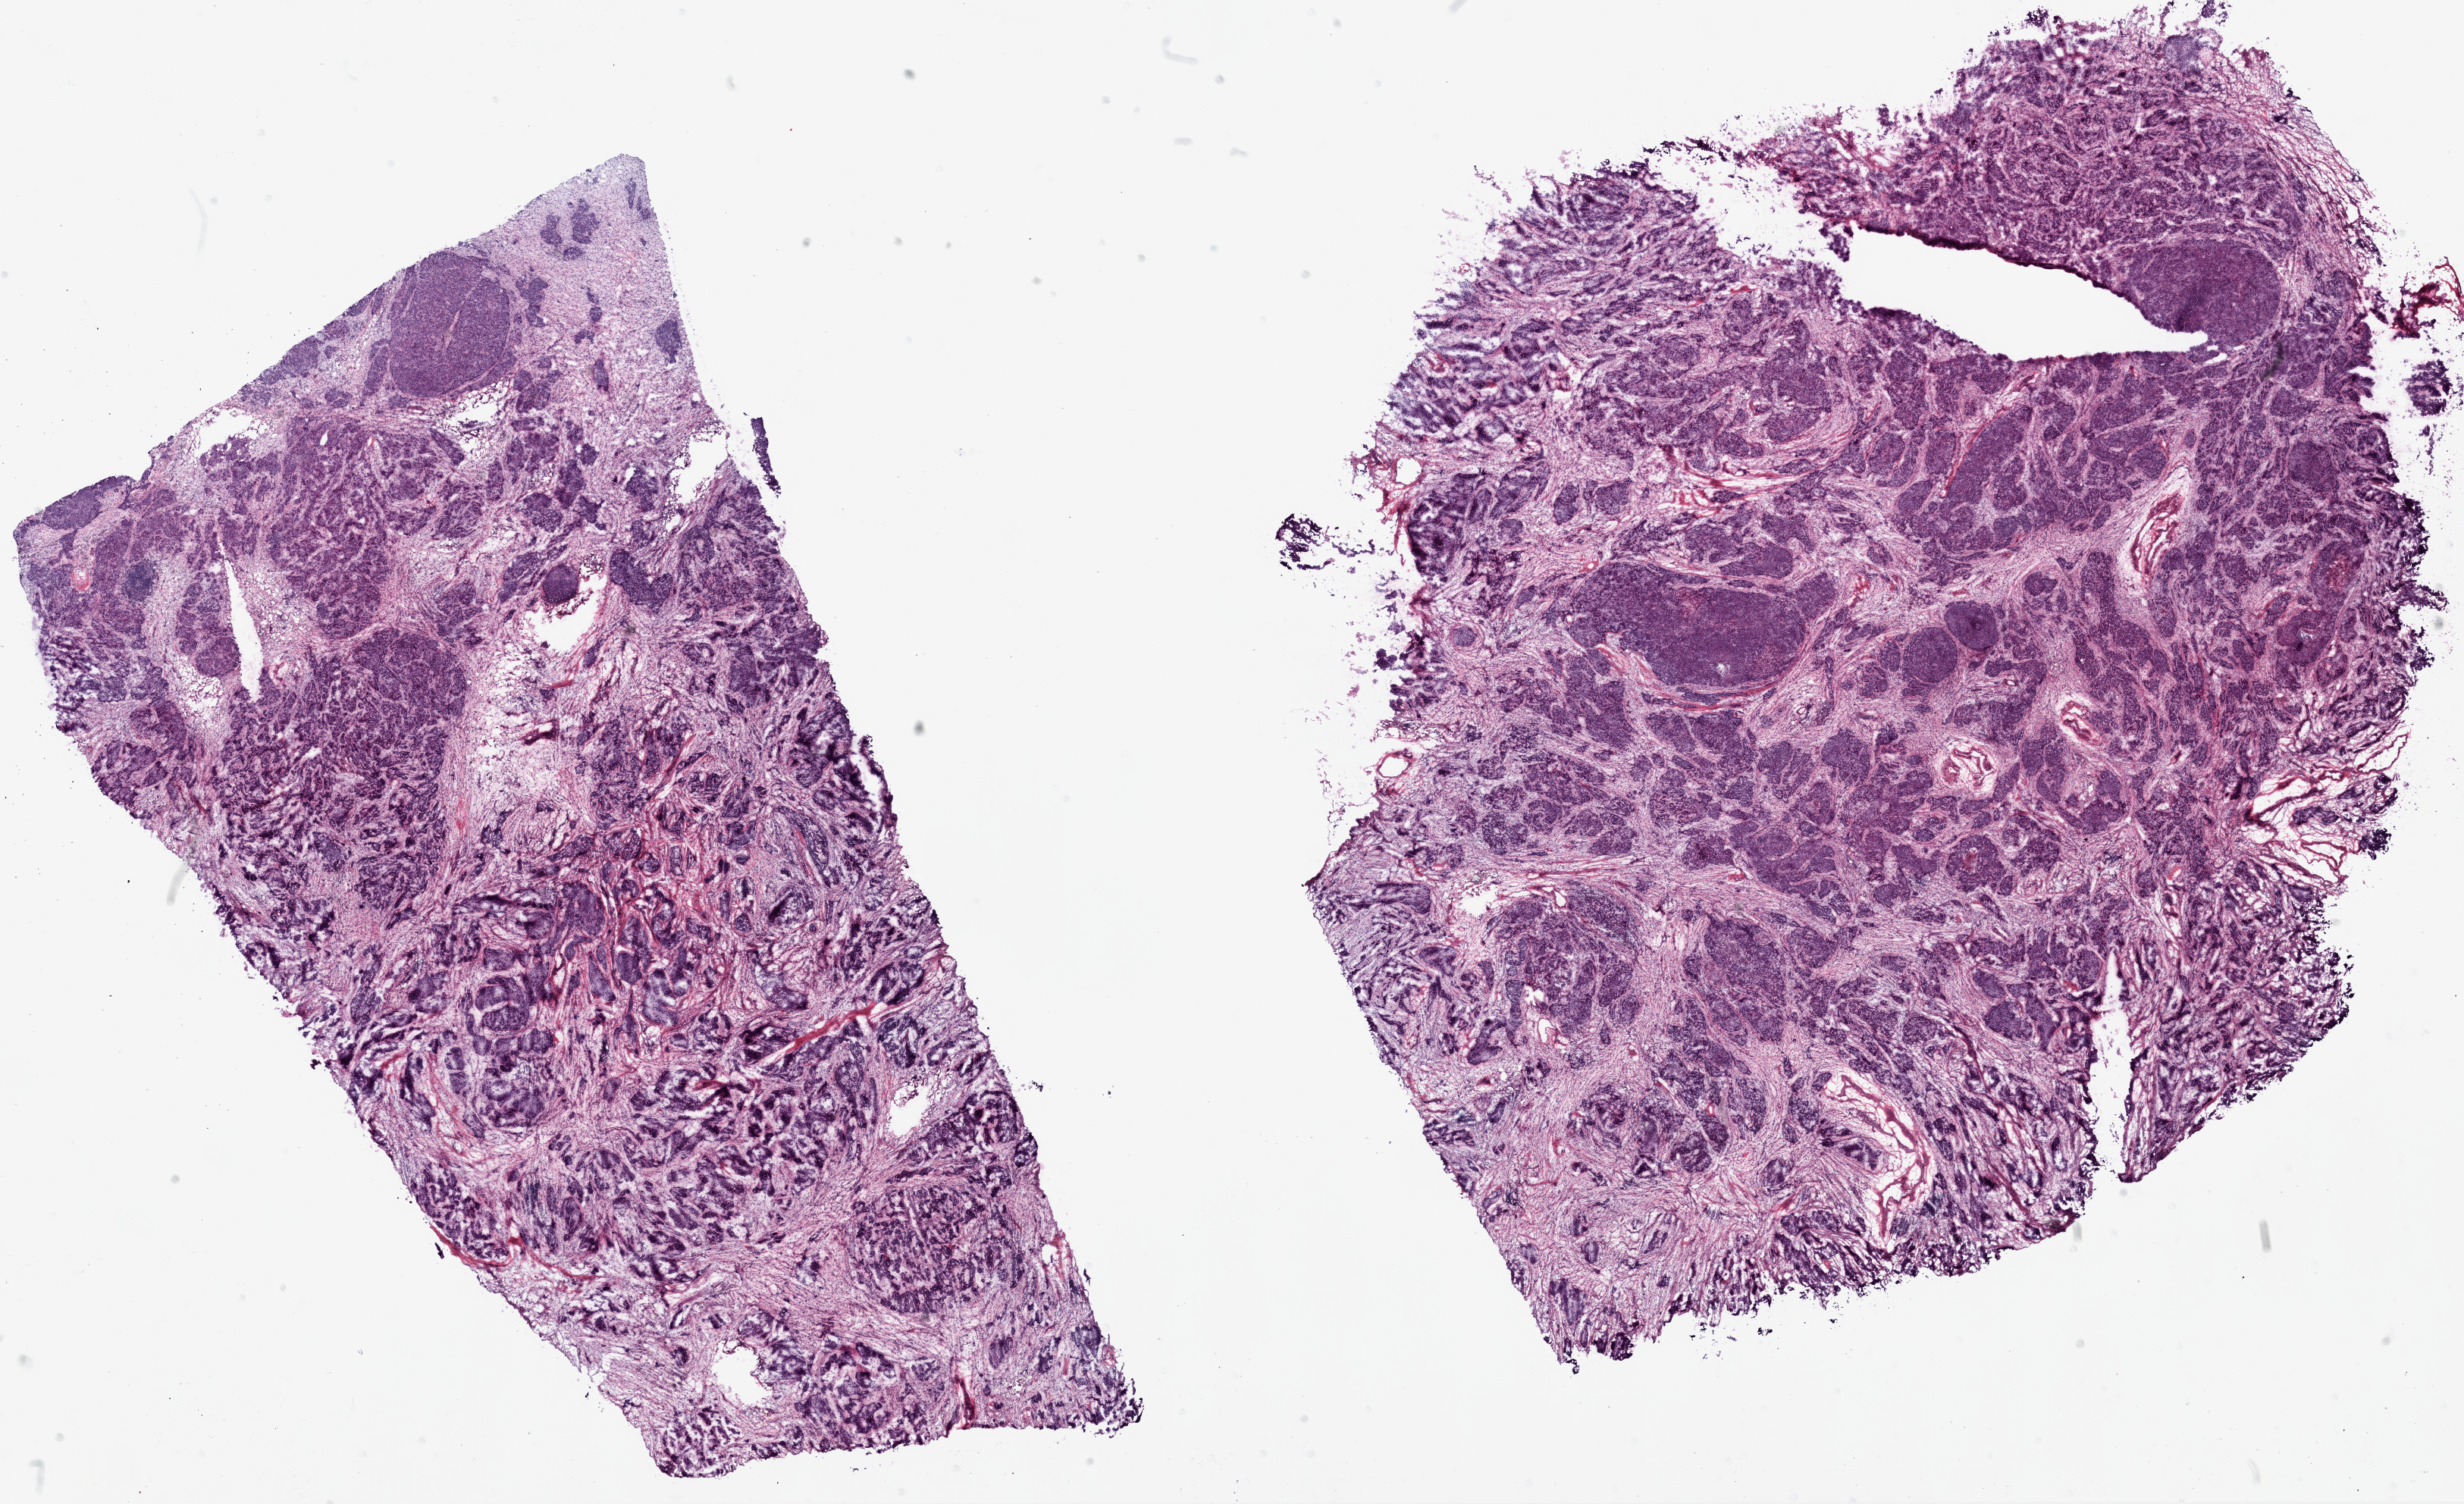
Whole-slide histology image, H&E-stained — shown as a low-resolution overview of the whole scanned area (about 26.1 x 15.9 mm, from a 20x scan), frozen section from the top of the tissue portion, ovary, primary tumour sample. Female, age 71 years at initial diagnosis. Histologic grade: G3 (poorly differentiated). Composition of this section per pathologist review: tumour cells 89%, tumour nuclei 90%, normal cells 0%, stromal cells 10%, necrosis 1%.
* FIGO stage: IIIC
* histologic diagnosis: Serous cystadenocarcinoma, NOS